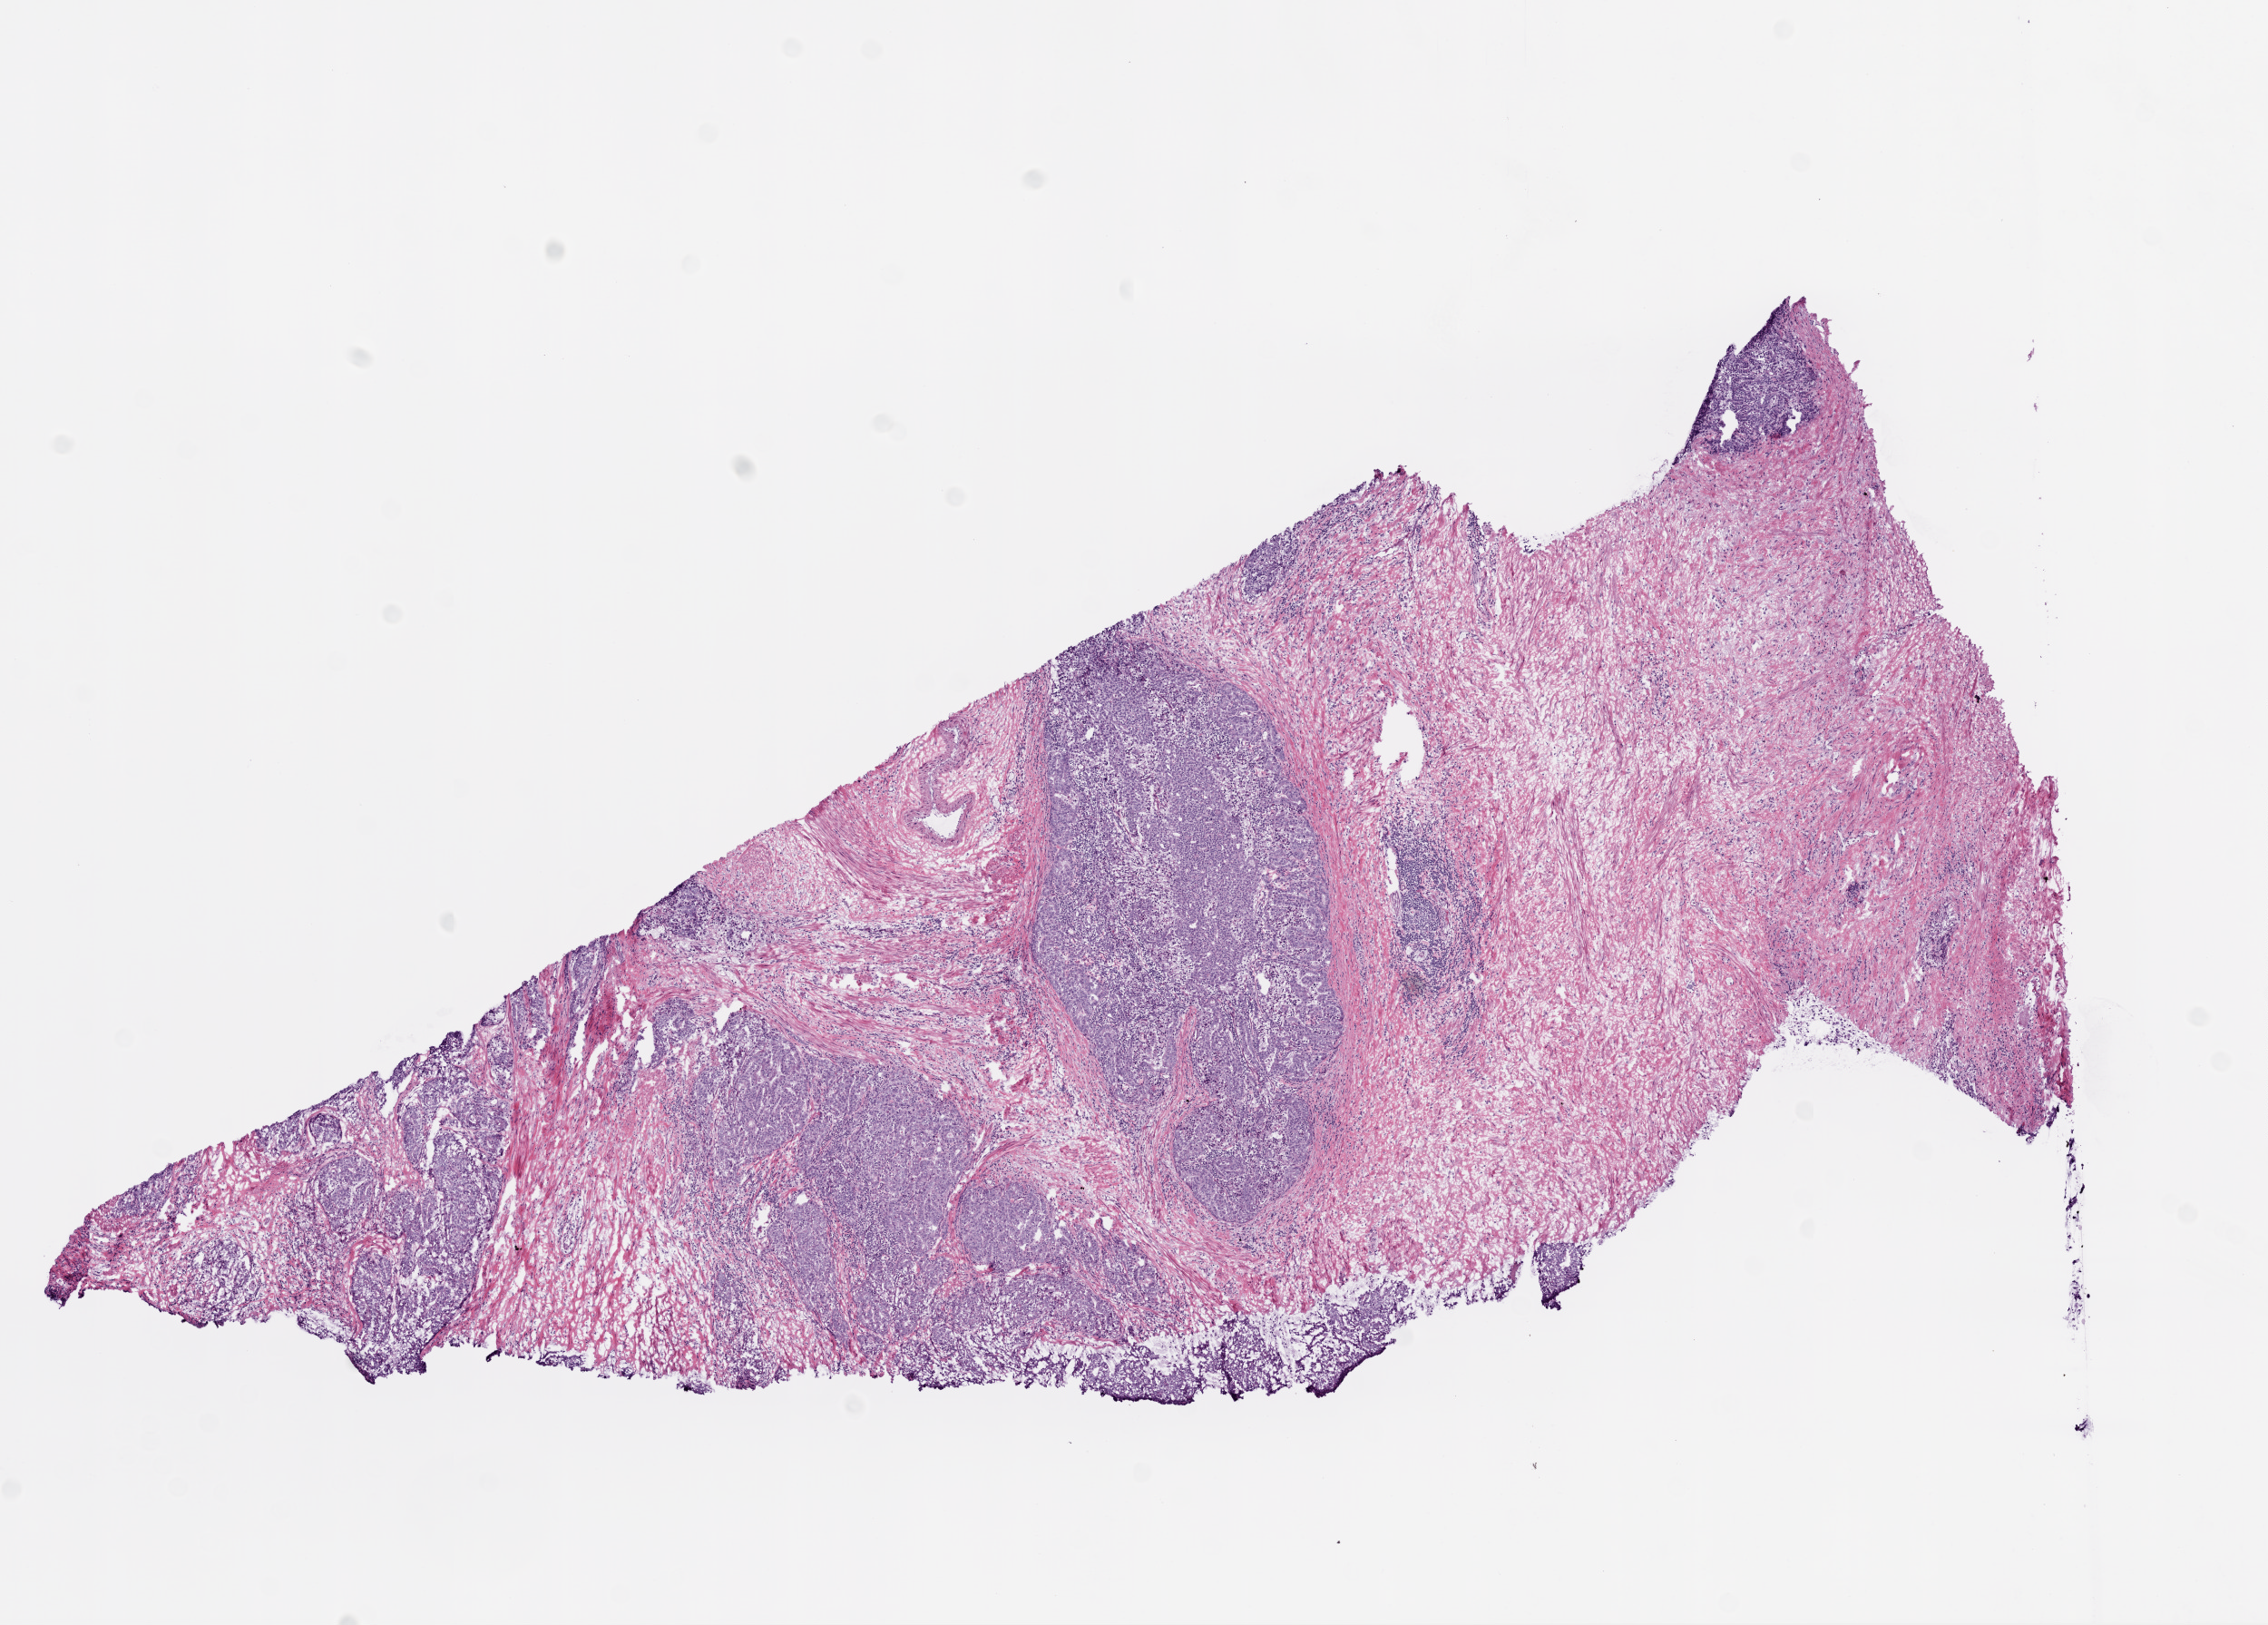
Whole-slide histology image, Hematoxylin and eosin (H&E) stained — shown as a low-resolution overview of the whole scanned area (about 10.0 x 7.2 mm, slide scanned at 20x), frozen section from the top of the tissue portion, prostate, primary tumour sample. Patient: male, age at initial diagnosis 65 years. Gleason score: 9 (4+5). Slide review estimates, as recorded: tumour cells 43%, tumour nuclei 60%, normal cells 0%, stromal cells 55%, necrosis 2%. Infiltration values recorded for this section: lymphocyte infiltration 3%, monocyte infiltration 2%, neutrophil infiltration 0%.
- histologic diagnosis: Acinar cell carcinoma
- laterality: bilateral